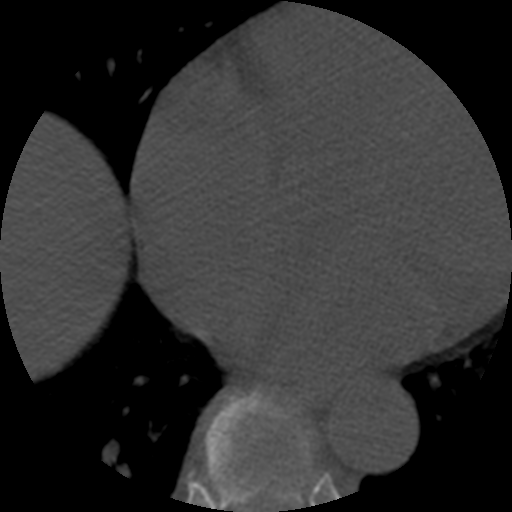
CT including the spine, one axial slice. Position 322 of 508 along the scan axis. Reconstruction kernel STANDARD. 120 kVp. Bone window (W 1800 / L 400 HU). 1.25 mm slice thickness. 512 × 512 image matrix, field of view 160 × 160 mm. Patient age 57 years. From the clinical record (not read from this slice): primary cancer: prostate.
Outlined on this slice (semi-automatic segmentation, software-assisted and operator-edited):
- T7 vertebra: bounding box (x1, y1, x2, y2) in pixels: (204, 392, 309, 512)
- T8 vertebra: (255, 407, 312, 505)